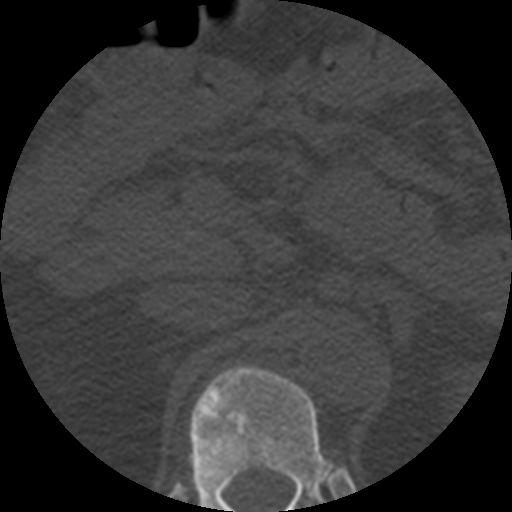
CT including the spine, one axial slice; slice 213 of 508 in the series (ordered by position); reconstruction kernel STANDARD; bone window (W 1800 / L 400 HU); 1.25 mm slice thickness; 512 × 512 image matrix, field of view 160 × 160 mm. Patient age 57 years. From the clinical record (not read from this slice): primary cancer: prostate.
Outlined on this slice (semi-automatic segmentation, software-assisted and operator-edited):
- T12 vertebra: box from (x=185, y=366) to (x=348, y=512) px